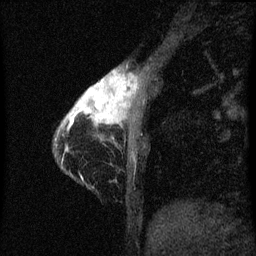
Breast MRI (dynamic contrast-enhanced), one sagittal slice; slice 10 of 60 in the series (ordered by position); dynamic contrast-enhanced series, image 2 of 3 at this slice position (ordered by acquisition); 1.5 T; TE 4.2 ms, TR 8 ms; 2 mm slice thickness; 256 × 256 image matrix, field of view 180 × 180 mm. Patient: female, 38 years.
Structures marked on this image (semi-automatically segmented with operator editing):
- analysis volume of interest (the breast-tissue region the enhancement analysis was run in; not a lesion): bounding box [x1, y1, x2, y2] px = [61, 70, 140, 147]
- tumour enhancement mask (voxels above the 70 % enhancement threshold inside the analysis volume of interest): [64, 70, 134, 125]